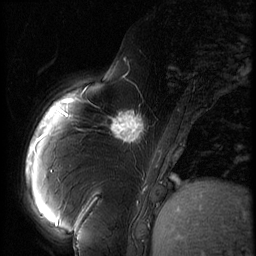
Breast MRI (dynamic contrast-enhanced), one sagittal slice. Slice 16 of 60 in the series (ordered by position). 3 images stored at this slice position (order not interpretable as contrast timing). 1.5 T. TE 4.2 ms, TR 9 ms. 2.5 mm slice thickness. 256 × 256 image matrix, field of view 180 × 180 mm. Patient: female, 57 years. From the clinical record (not read from this slice): setting: breast cancer imaged before/during neoadjuvant chemotherapy; receptor status: triple-negative.
Annotated regions visible in this slice (semi-automatic segmentation, software-assisted and operator-edited):
- analysis volume of interest (the breast-tissue region the enhancement analysis was run in; not a lesion): bounding box [x1, y1, x2, y2] px = [106, 101, 157, 152]
- tumour enhancement mask (voxels above the 140 % enhancement threshold inside the analysis volume of interest): [110, 112, 145, 143]